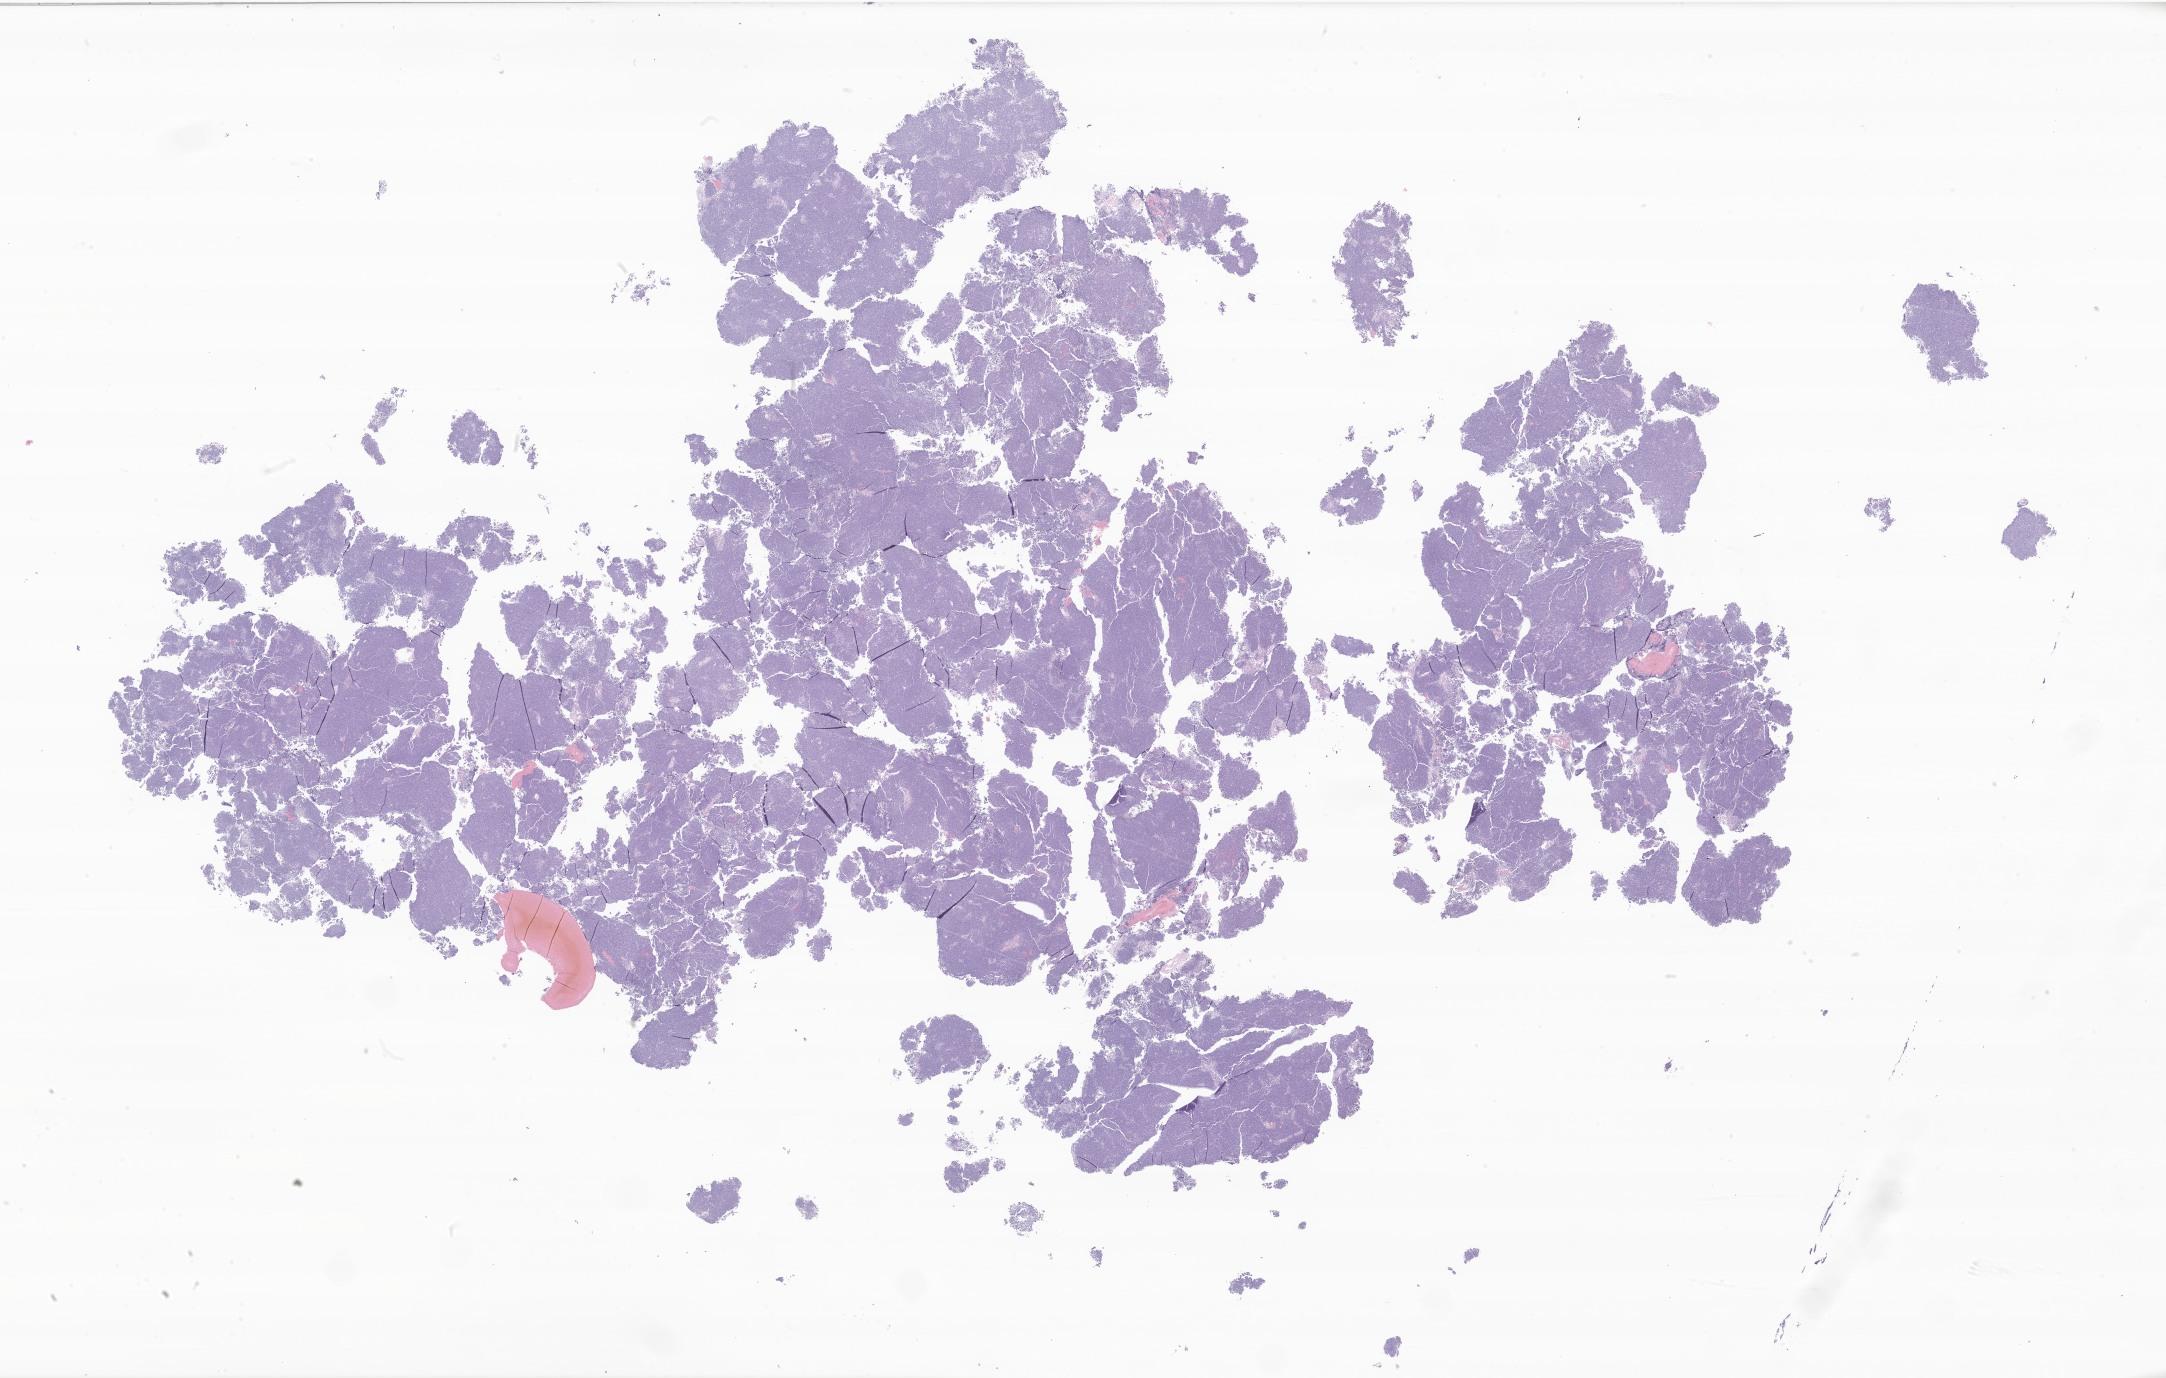
Whole-slide image, H&E stain of tumor tissue from the brain stem — a low-resolution overview of the entire scanned area, about 36.5 x 23.2 mm; formalin-fixed, paraffin-embedded (FFPE) tissue. Patient: male, age 92 months.
Diagnosis: Medulloblastoma, NOS.